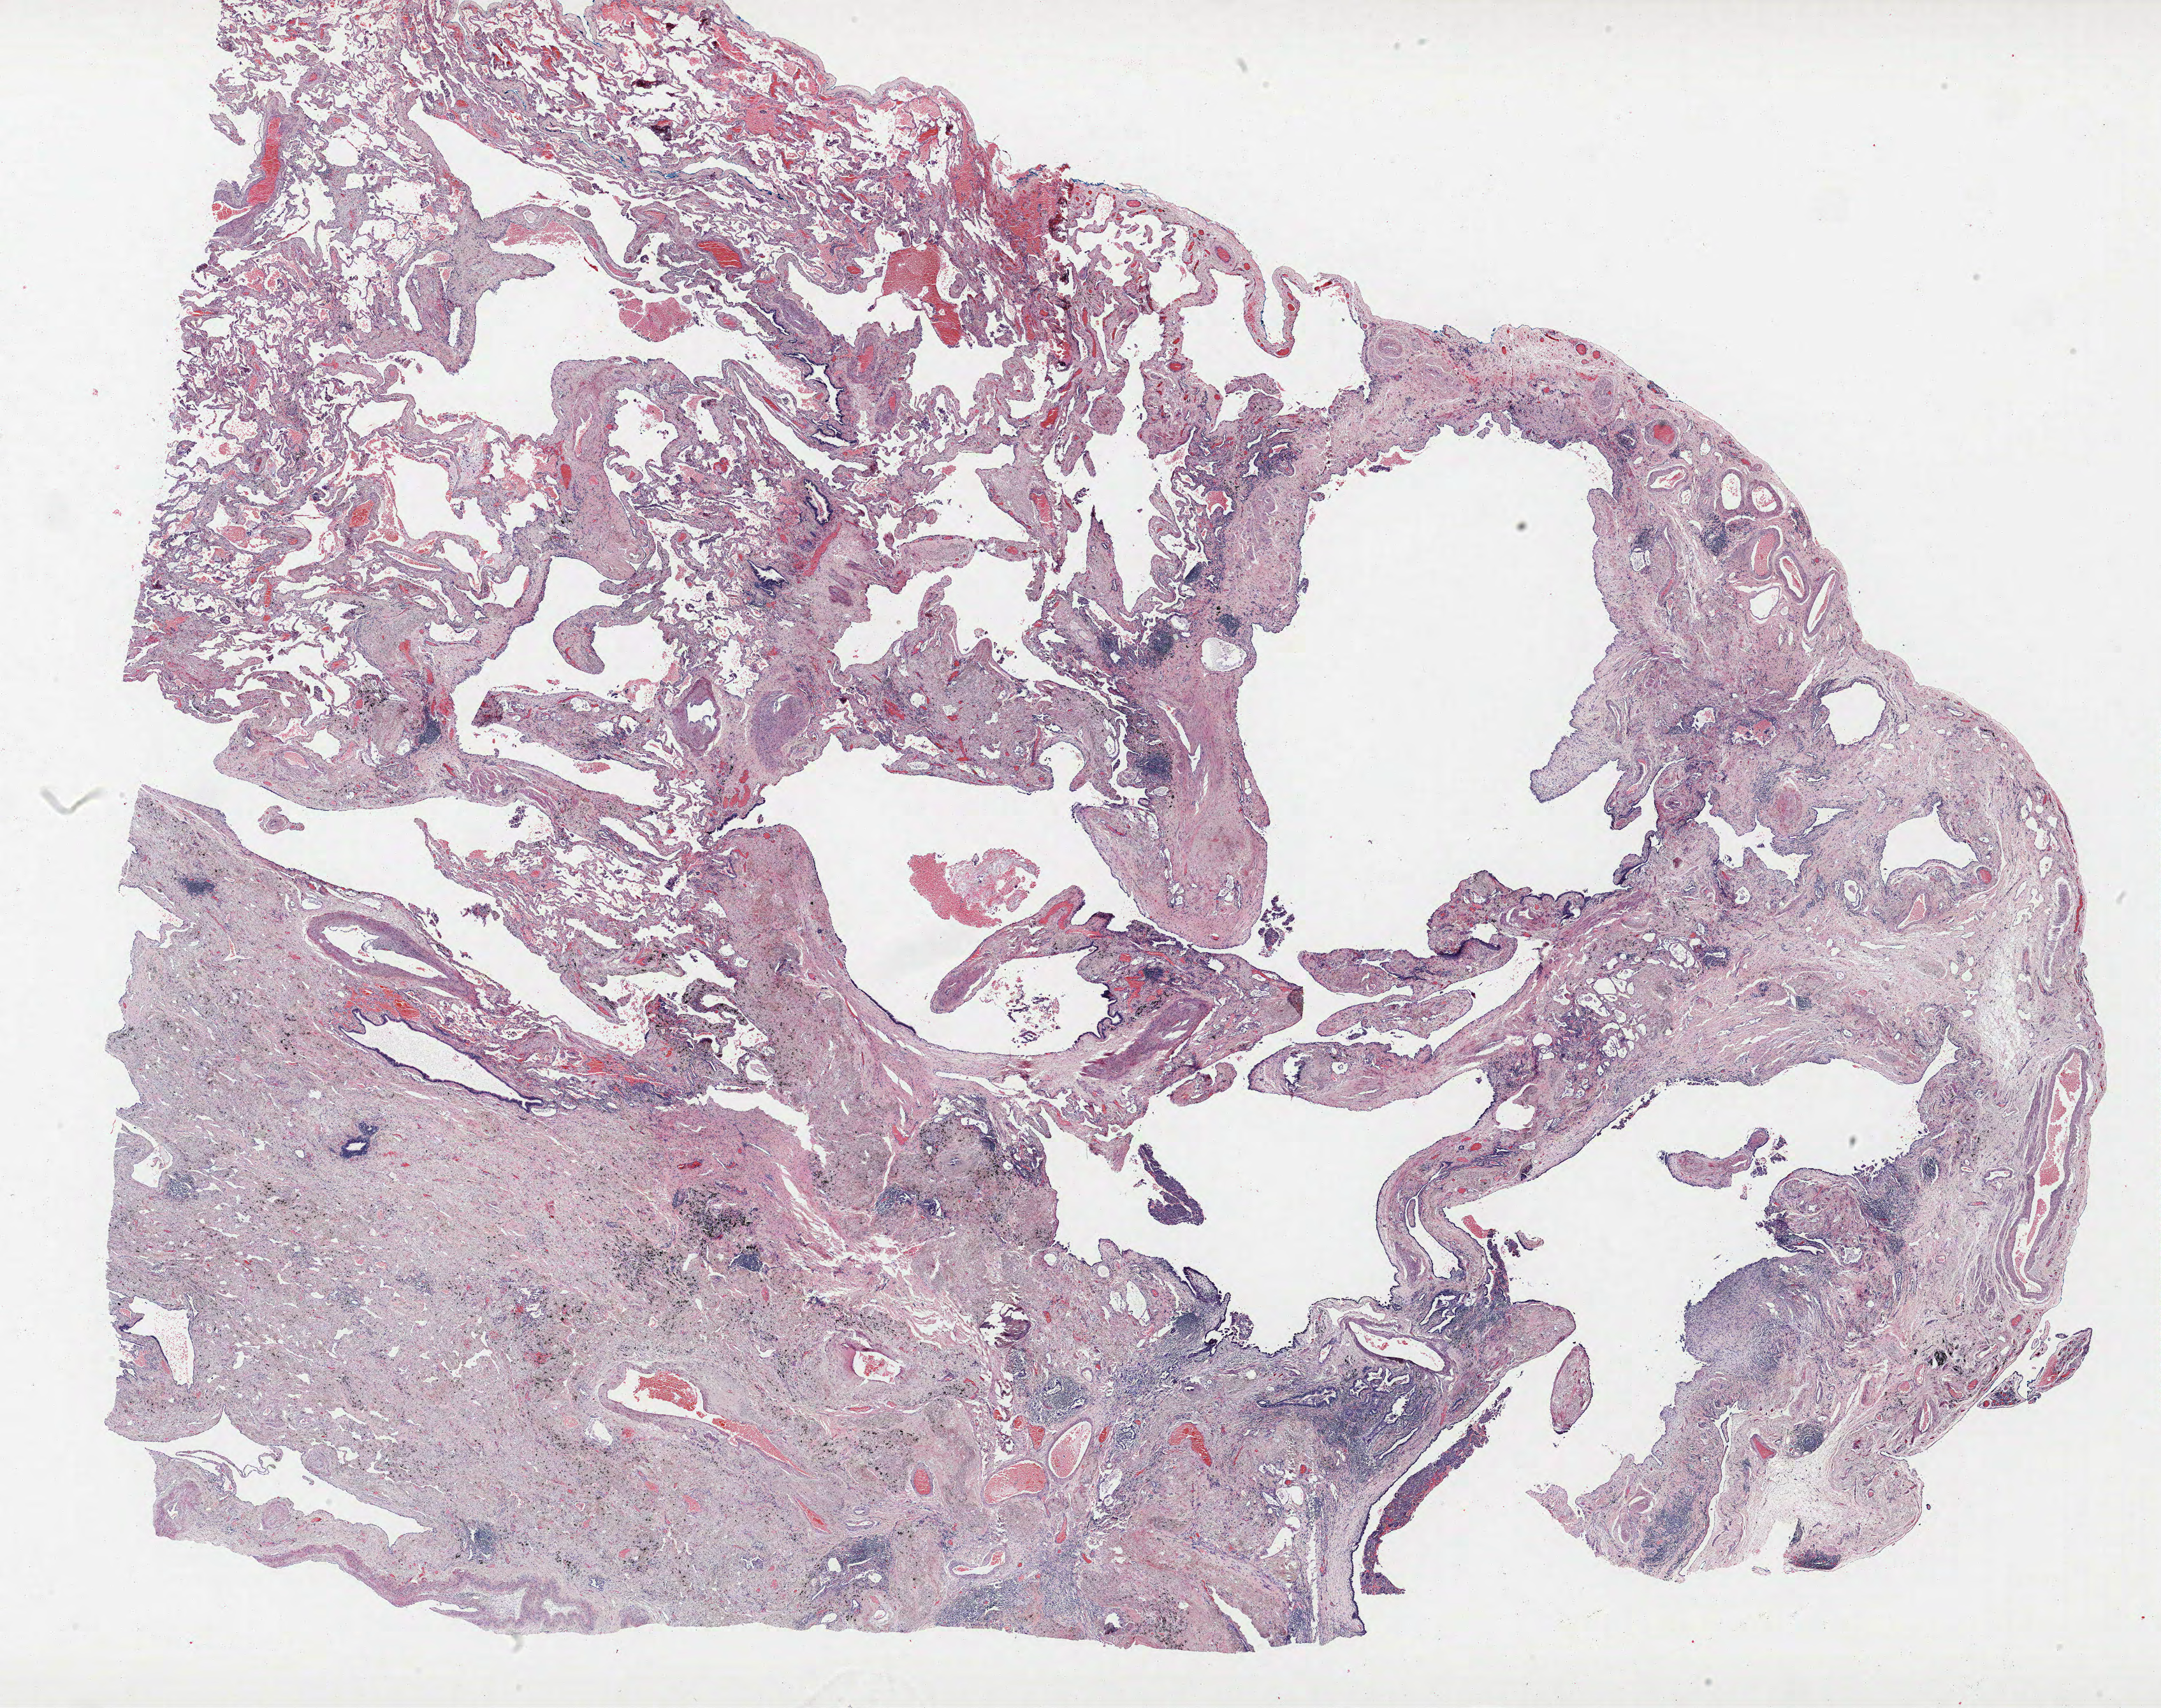
H&E whole-slide image — shown as a low-resolution overview of the whole scanned area (about 27.1 x 21.4 mm, acquisition: 40x scan); formalin-fixed paraffin-embedded (FFPE) section; lung. Male, age 67 at enrolment. Grade: moderately differentiated (G2).
- ICD-O-3 topography: upper lobe of lung (C34.1)
- participant's lung-cancer diagnosis: Adenocarcinoma, NOS (ICD-O-3 8140/3)
- stage (AJCC 6th edition): IB
- tumour size (pathology): 40 mm
- primary tumour location (clinical record): left upper lobe